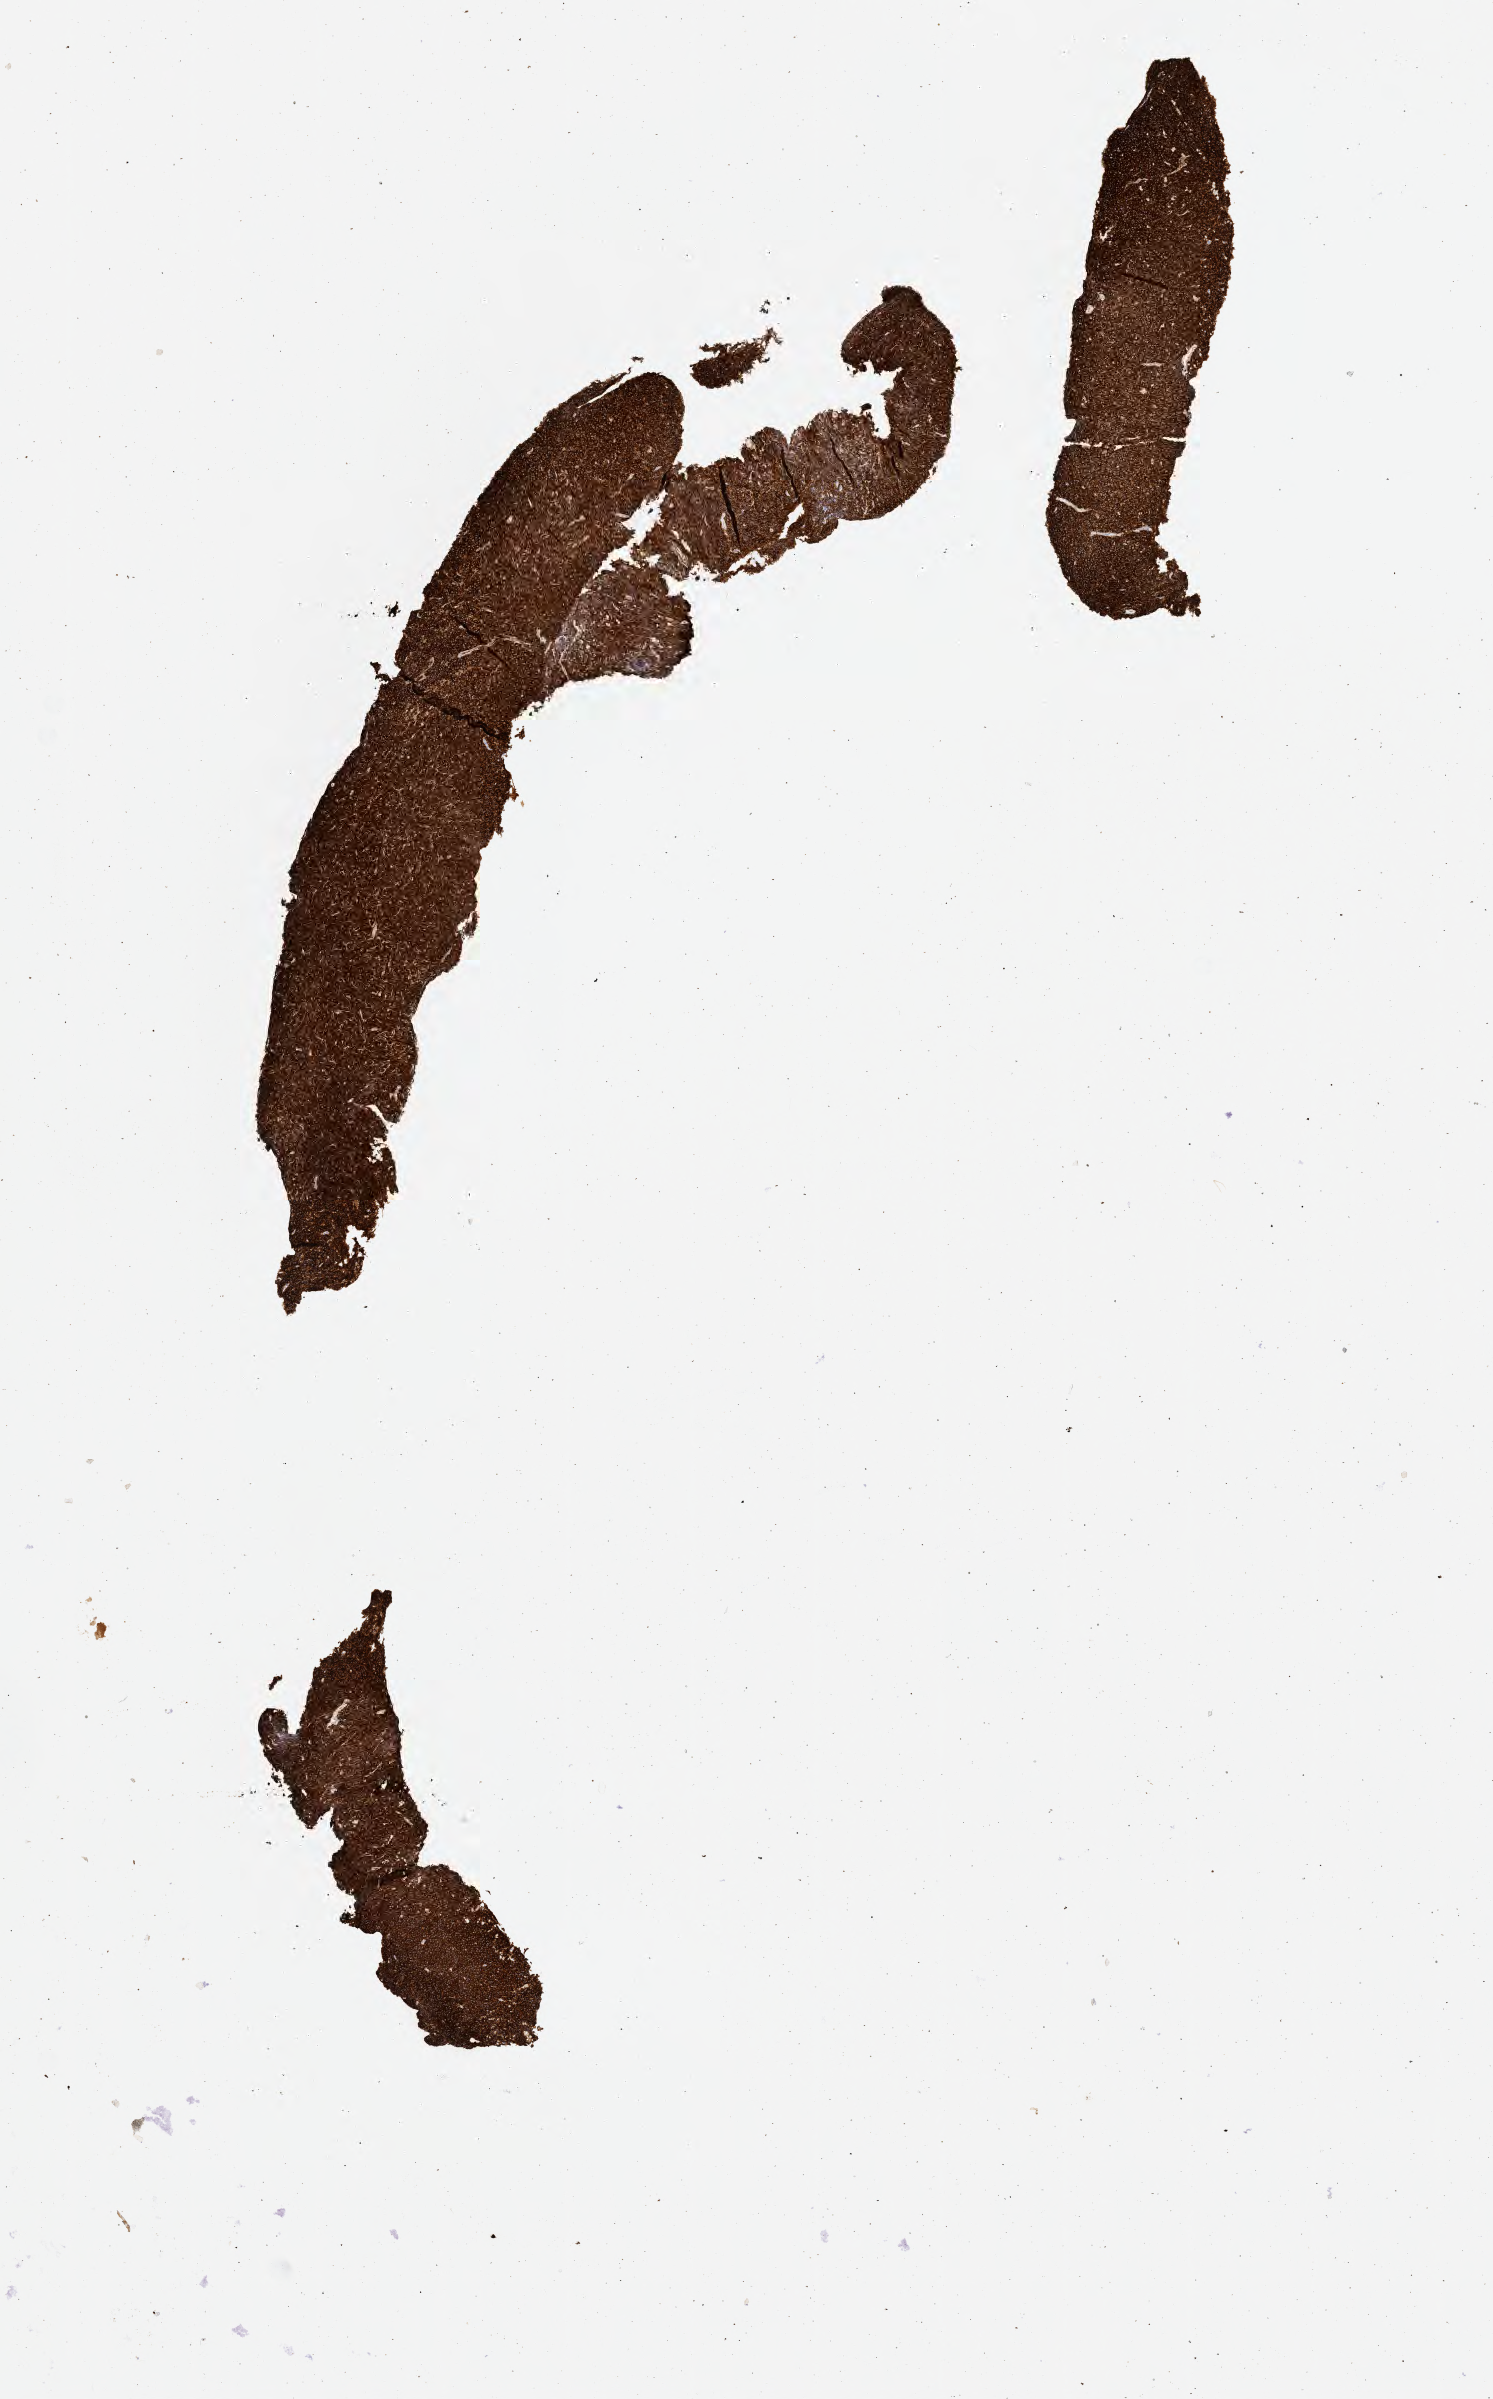
IHC for CD20, whole-slide image — shown as a low-resolution overview of the whole scanned area (about 6.0 x 9.7 mm); specimen: tumor tissue. Male patient, 10 years old.
Histologic diagnosis: Diffuse large B-cell lymphoma, NOS.